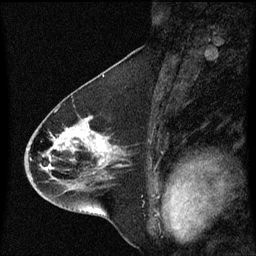
Breast MRI (dynamic contrast-enhanced), one sagittal slice. Slice 33 of 60 in the series (ordered by position). Dynamic contrast-enhanced series, image 2 of 3 at this slice position (ordered by acquisition). 1.5 T. TE 4.2 ms, TR 8.4 ms. 2 mm slice thickness. 256 × 256 image matrix. Patient: female, 46 years. From the clinical record (not read from this slice): setting: breast cancer imaged before/during neoadjuvant chemotherapy; receptor status: HER2-positive.
Outlined on this slice (semi-automatic segmentation, software-assisted and operator-edited):
- analysis volume of interest (the breast-tissue region the enhancement analysis was run in; not a lesion): bounding box <25,112,125,195> (left, top, right, bottom; pixels)
- tumour enhancement mask (voxels above the 70 % enhancement threshold inside the analysis volume of interest): <51,134,107,159>